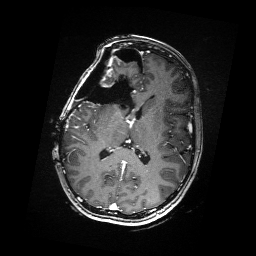
Brain MRI from a brain-tumour surgery series, one axial slice. T1-weighted post-contrast. 1 mm slice thickness. 256 × 256 image matrix, field of view 256 × 256 mm. From the clinical record (not read from this slice): histopathology: Metastatic Carcinoma from Breast primary.
Annotated regions visible in this slice (manually delineated by an expert):
- residual tumour: bounding box [x1, y1, x2, y2] px = [94, 68, 112, 87]